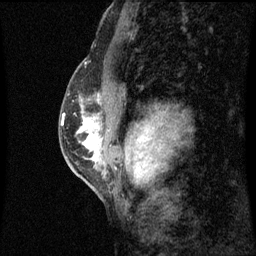
Breast MRI (dynamic contrast-enhanced), one sagittal slice. Slice 35 of 60 in the series (ordered by position). Dynamic contrast-enhanced series, image 2 of 3 at this slice position (ordered by acquisition). 1.5 T. TE 4.2 ms, TR 8.9 ms. 256 × 256 image matrix, field of view 200 × 200 mm. Female patient, age 50 years. From the clinical record (not read from this slice): setting: breast cancer imaged before/during neoadjuvant chemotherapy; receptor status: triple-negative.
Outlined on this slice (semi-automatically segmented with operator editing):
- analysis volume of interest (the breast-tissue region the enhancement analysis was run in; not a lesion): bounding box (x1, y1, x2, y2) in pixels: (68, 80, 103, 169)
- tumour enhancement mask (voxels above the 70 % enhancement threshold inside the analysis volume of interest): (82, 118, 99, 163)